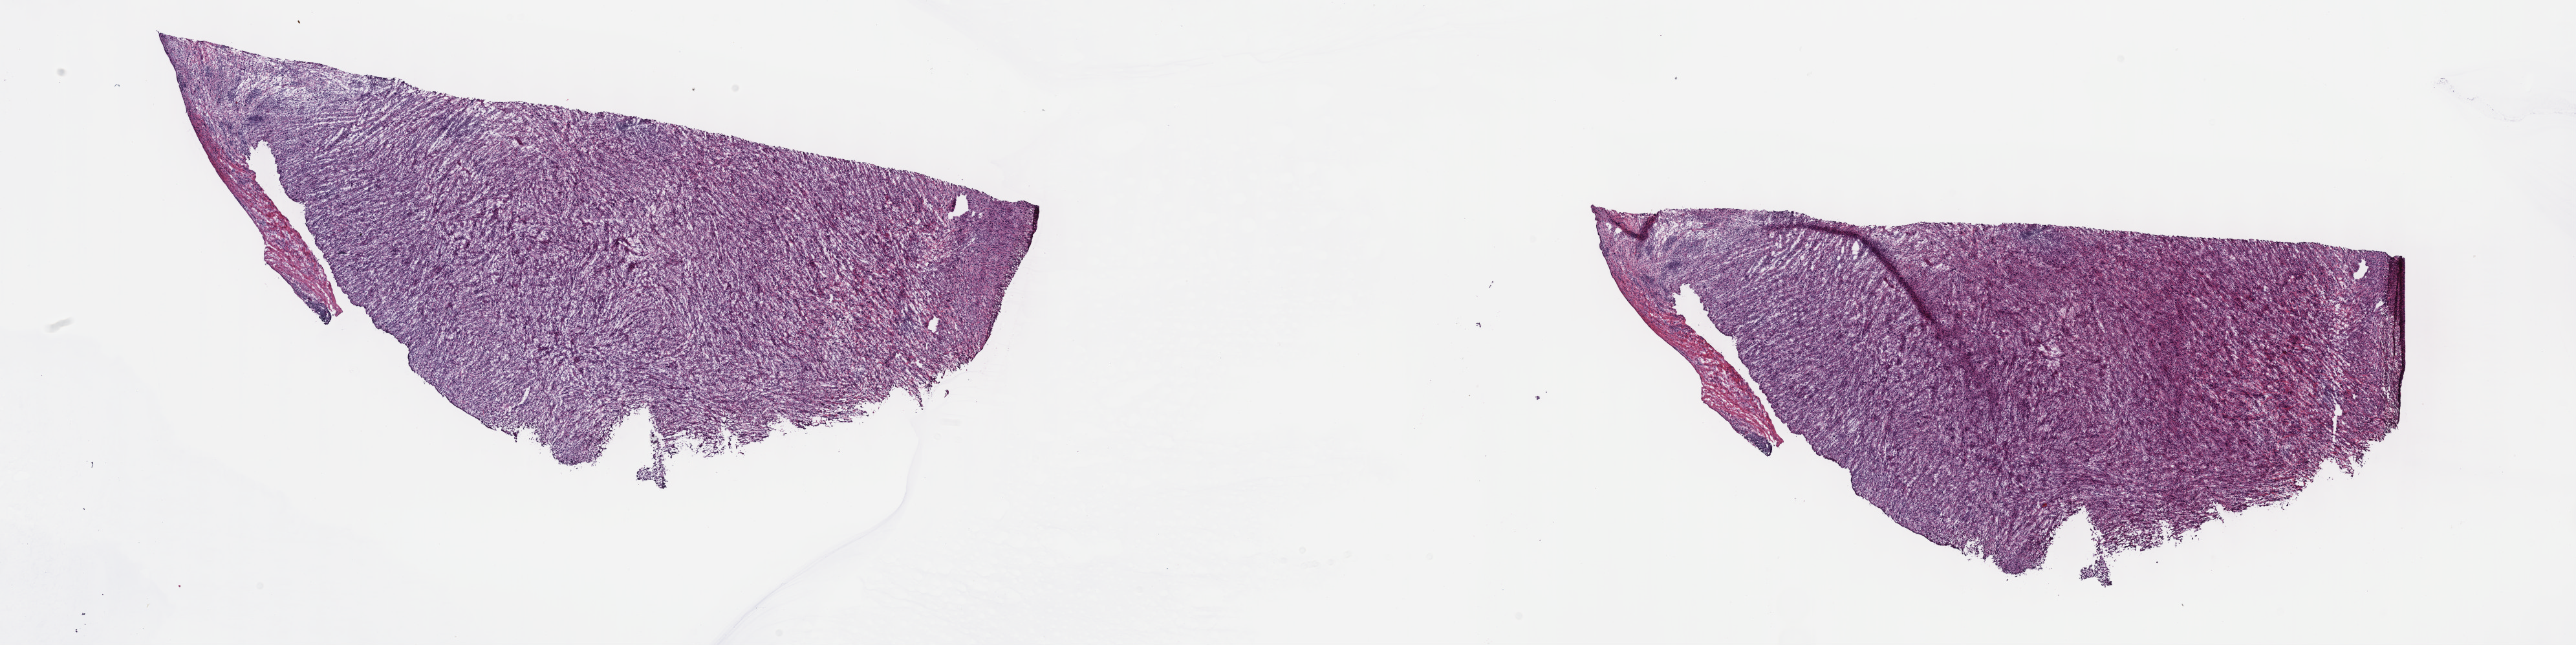
H&E-stained whole-slide image — whole scanned area (about 32.2 x 8.1 mm, acquisition: 40x scan) shown as a low-resolution overview, frozen section from the top of the tissue portion, connective, subcutaneous and other soft tissues, primary tumour sample. Male patient; age at initial diagnosis 59 years. Slide review estimates, as recorded: tumour cells 100%, tumour nuclei 80%, normal cells 0%, stromal cells 0%, necrosis 0%. Inflammatory infiltration, as recorded: lymphocyte infiltration 2%, monocyte infiltration 0%, neutrophil infiltration 0%.
• diagnosis: Undifferentiated sarcoma